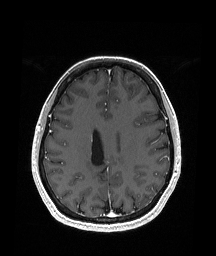
Brain MRI from a brain-tumour surgery series, one axial slice; slice 74 of 151 in the series (ordered by position); T1-weighted post-contrast; 216 × 256 image matrix, field of view 211 × 250 mm. Case-level facts recorded for this patient, not image findings: histopathology: Oligodendroglioma; WHO grade: 2; IDH mutation: yes; tumour location: Right Parietal.
Structures marked on this image (manually delineated by an expert):
- previous resection cavity: bounding box (x1, y1, x2, y2) in pixels: (94, 155, 109, 173)